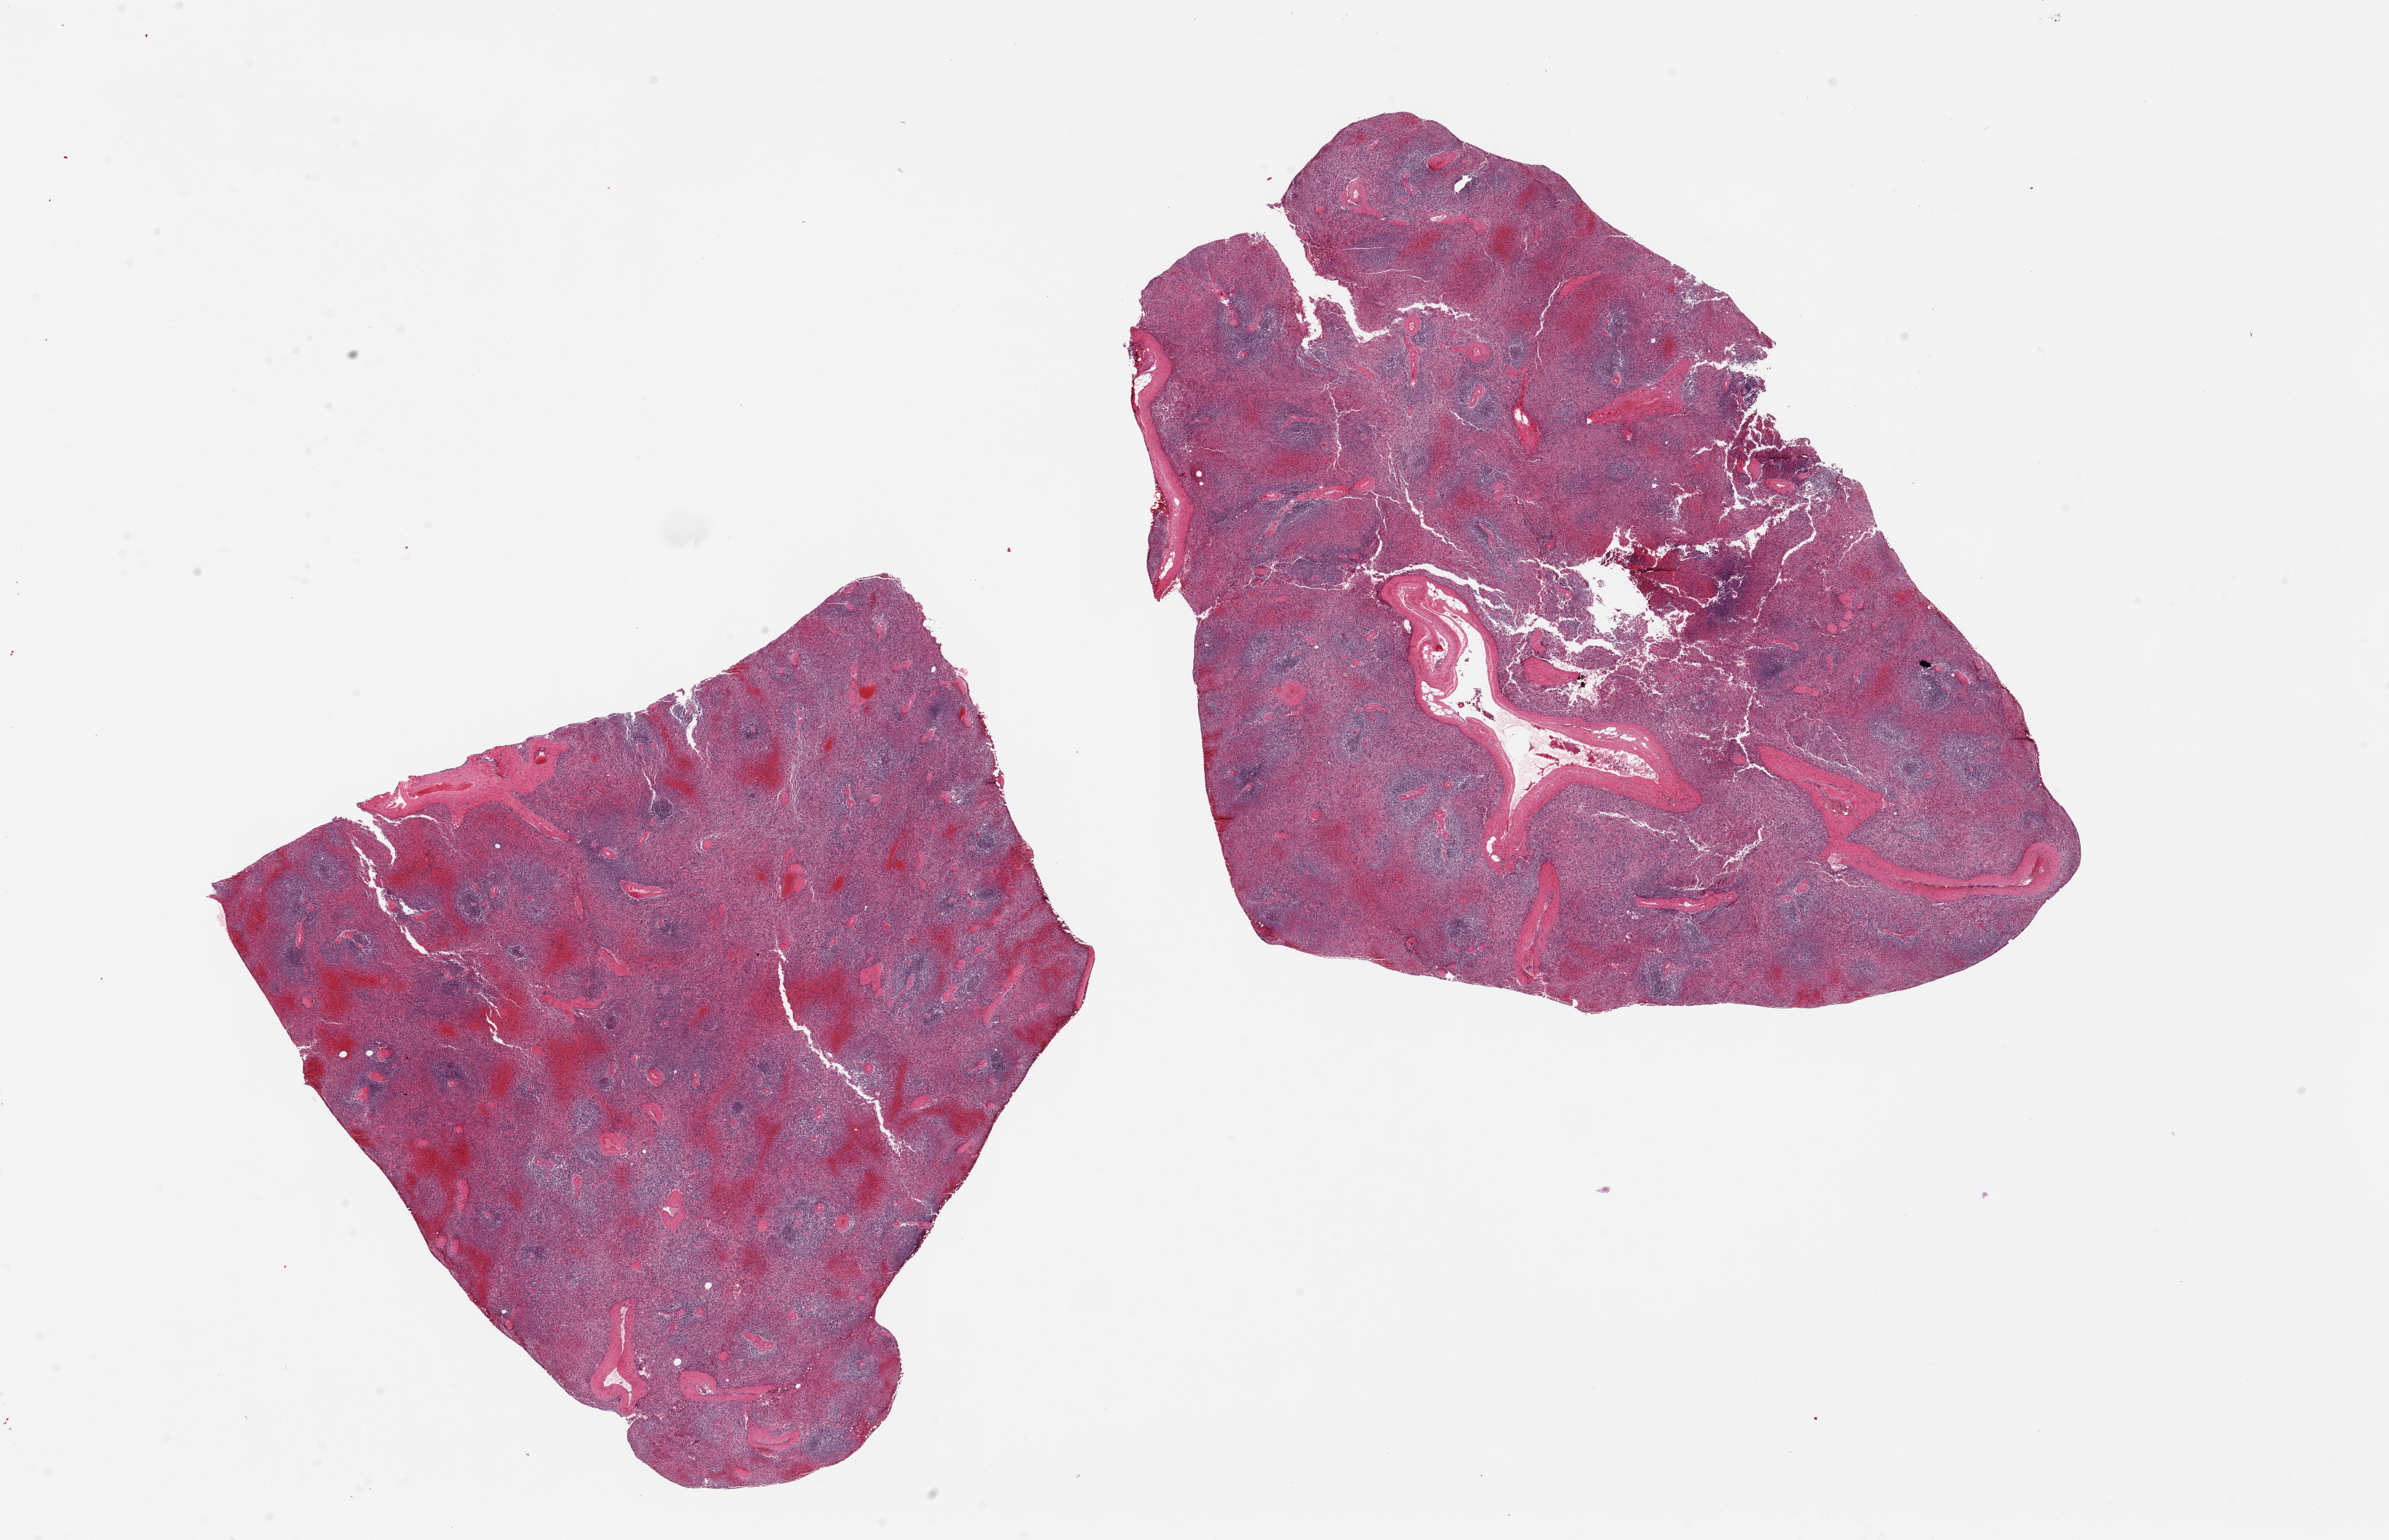
Digitized H&E-stained section — a low-resolution overview of the entire scanned area, about 30.5 x 19.7 mm (from a 20x scan), PAXgene-fixed, paraffin-embedded tissue, target tissue: spleen, donor tissue sample. Donor sex: female.
Pathologist's review note for this sample: 2 pieces, 11x10 & 13x11mm.